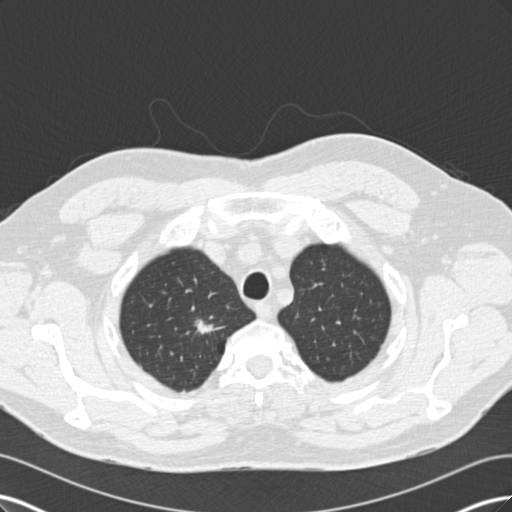
Low-dose screening chest CT, axial slice; first (baseline) screen; lung window (W 1500 / L -600 HU); standard (soft-tissue) reconstruction kernel (B30f); 512 × 512 image matrix, field of view 360 × 360 mm. Male, age 56 years at enrolment.
- Lesion marked by an expert reader, box from (x=174, y=308) to (x=225, y=352) px.
- The exam's reader record, not a measurement of the box and not confirmed to be the same lesion: non-calcified nodule or mass ≥4 mm, right upper lobe, 14 × 8 mm, spiculated (stellate) margins.
- Official screen result: positive, change unspecified: nodule(s) >= 4 mm or enlarging nodule(s), mass(es), or other non-specific abnormalities suspicious for lung cancer.